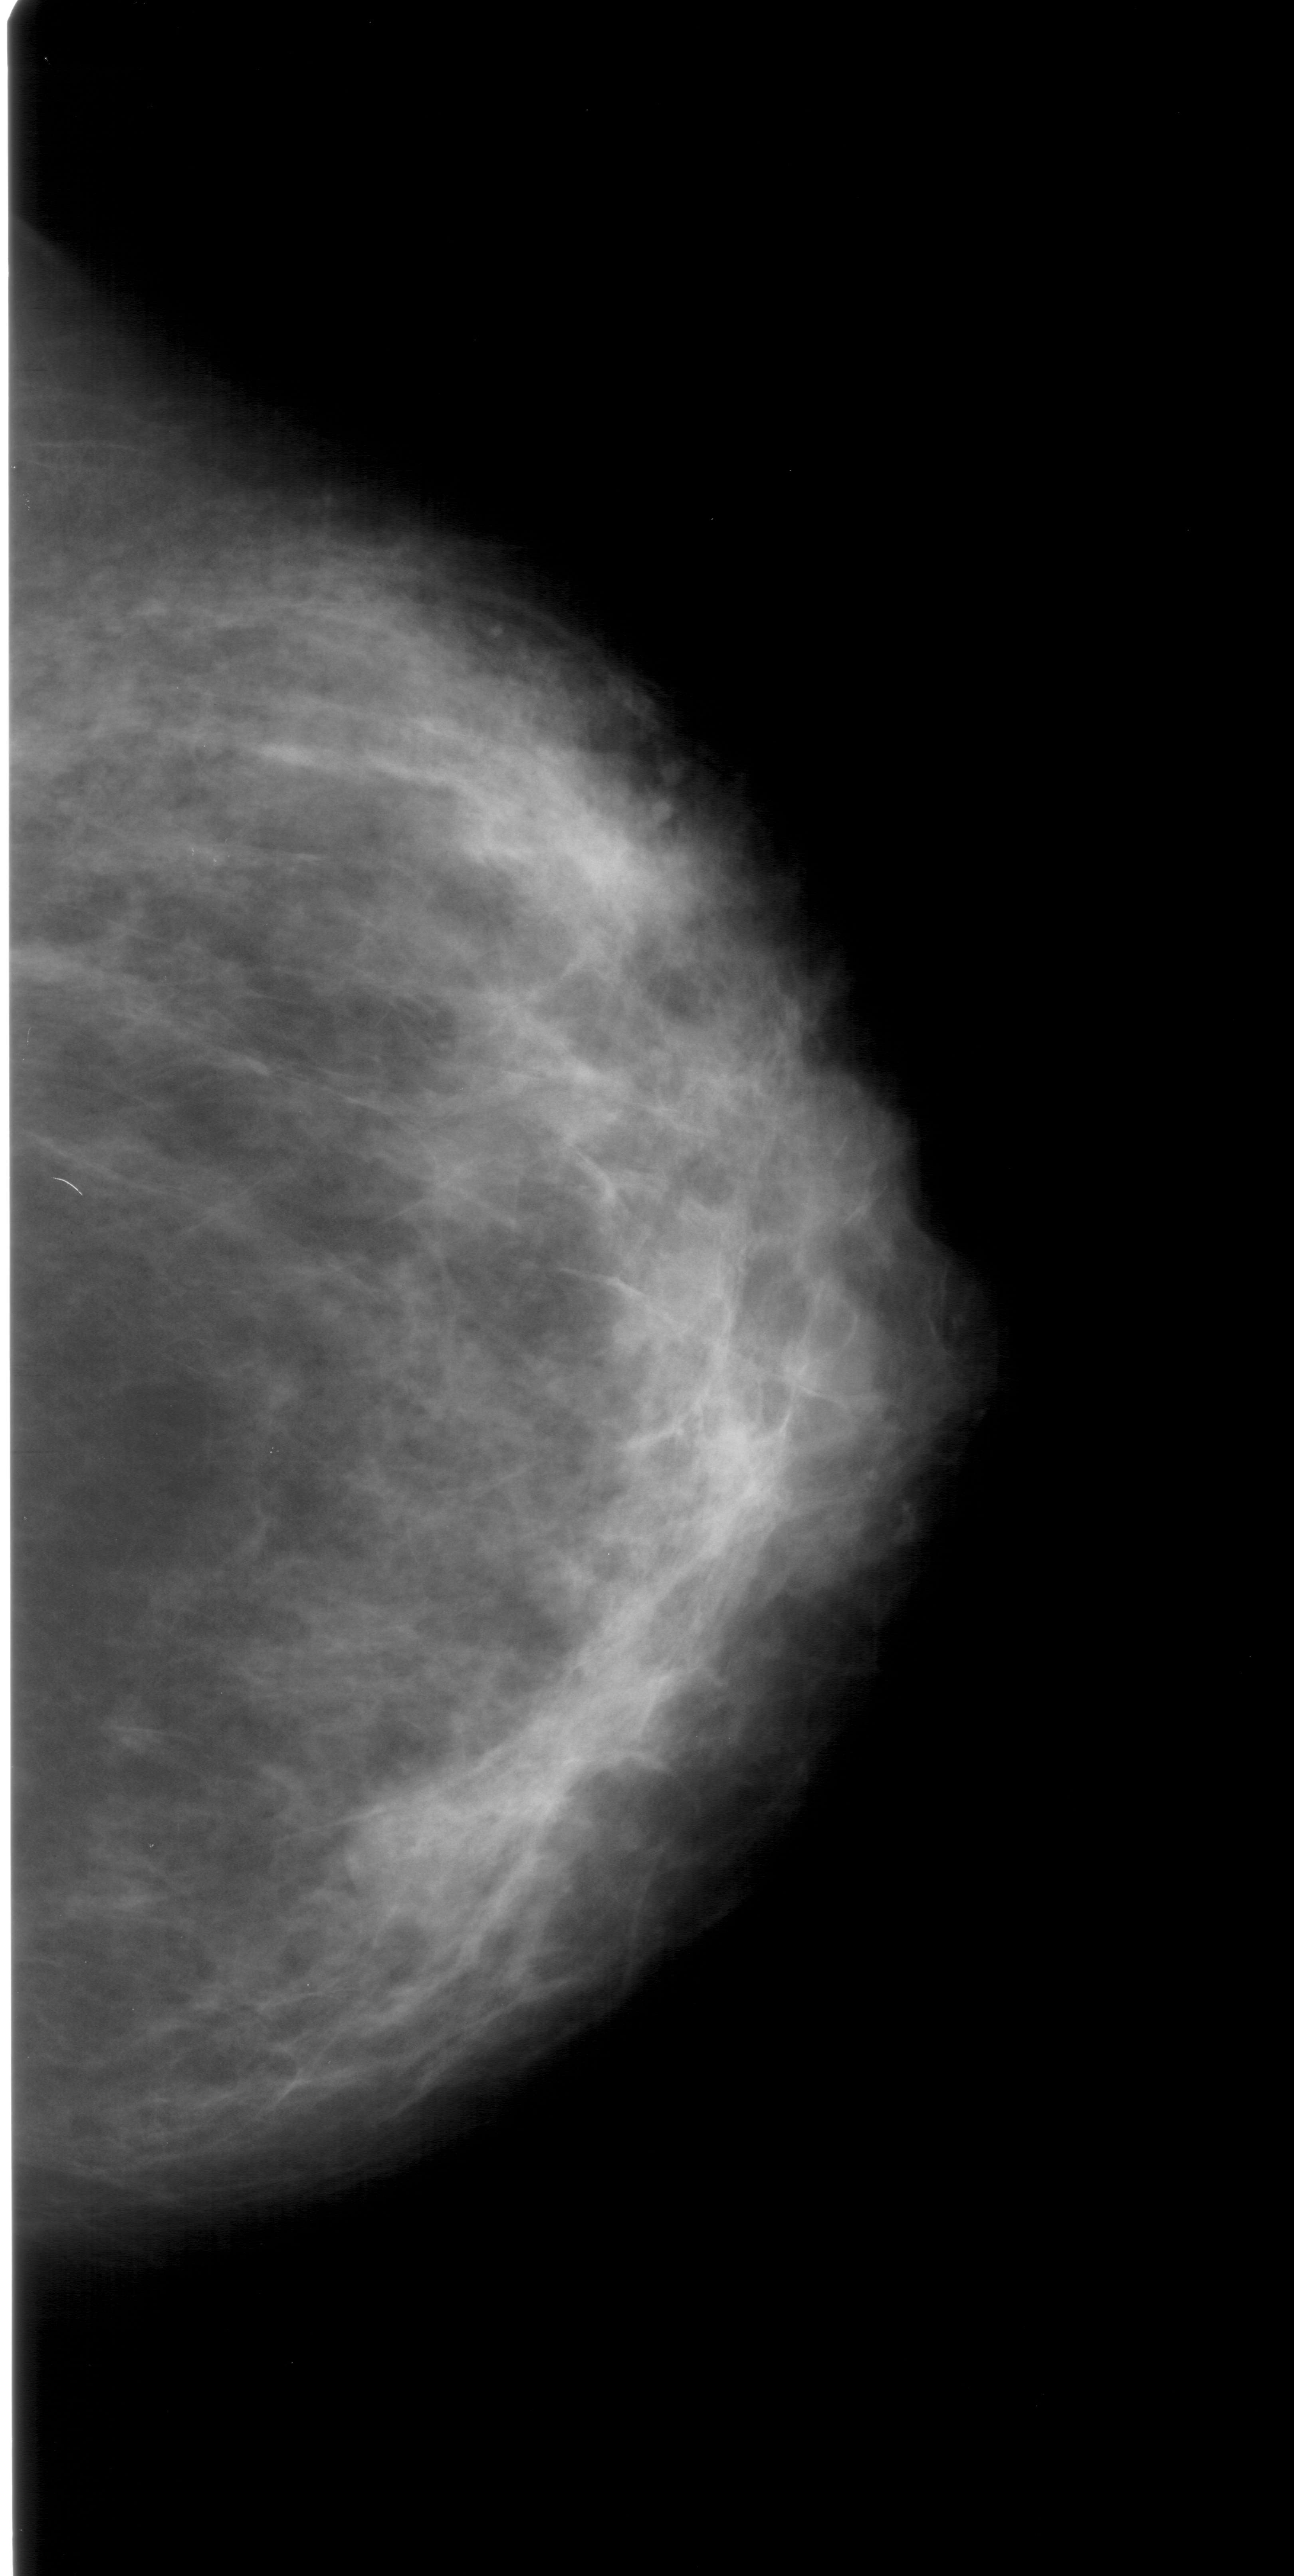
Scanned film-screen mammogram; right breast; CC view; BI-RADS breast density category 3 (scale 1–4); 1294 × 2576 image matrix.
Expert-marked regions of interest on this film, with their recorded descriptors:
- mass, shape round, margins obscured; BI-RADS assessment category 4; pathology (as recorded): benign: bounding box (x1, y1, x2, y2) in pixels: (389, 1774, 549, 1924)